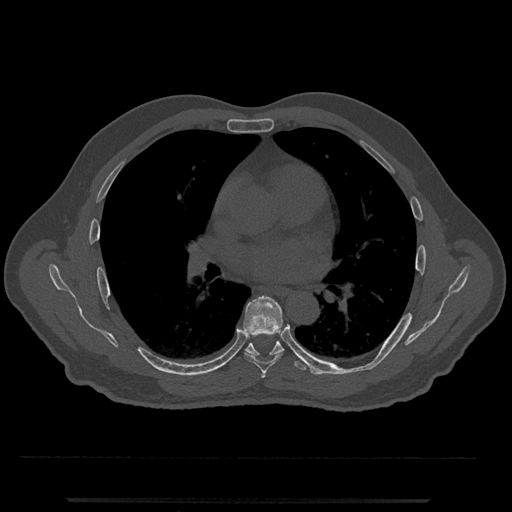
CT including the spine, one axial slice. Position 716 of 797 along the scan axis. Reconstruction kernel Br40s/3. Bone window (W 1800 / L 400 HU). 512 × 512 image matrix, field of view 419 × 419 mm. Patient: male, 63 years. Case-level facts recorded for this patient, not image findings: primary cancer: prostate.
Annotated regions visible in this slice (semi-automatically segmented with operator editing):
- T5 vertebra: bounding box <261,372,266,378> (left, top, right, bottom; pixels)
- T6 vertebra: <243,295,283,373>
- T7 vertebra: <224,340,326,375>